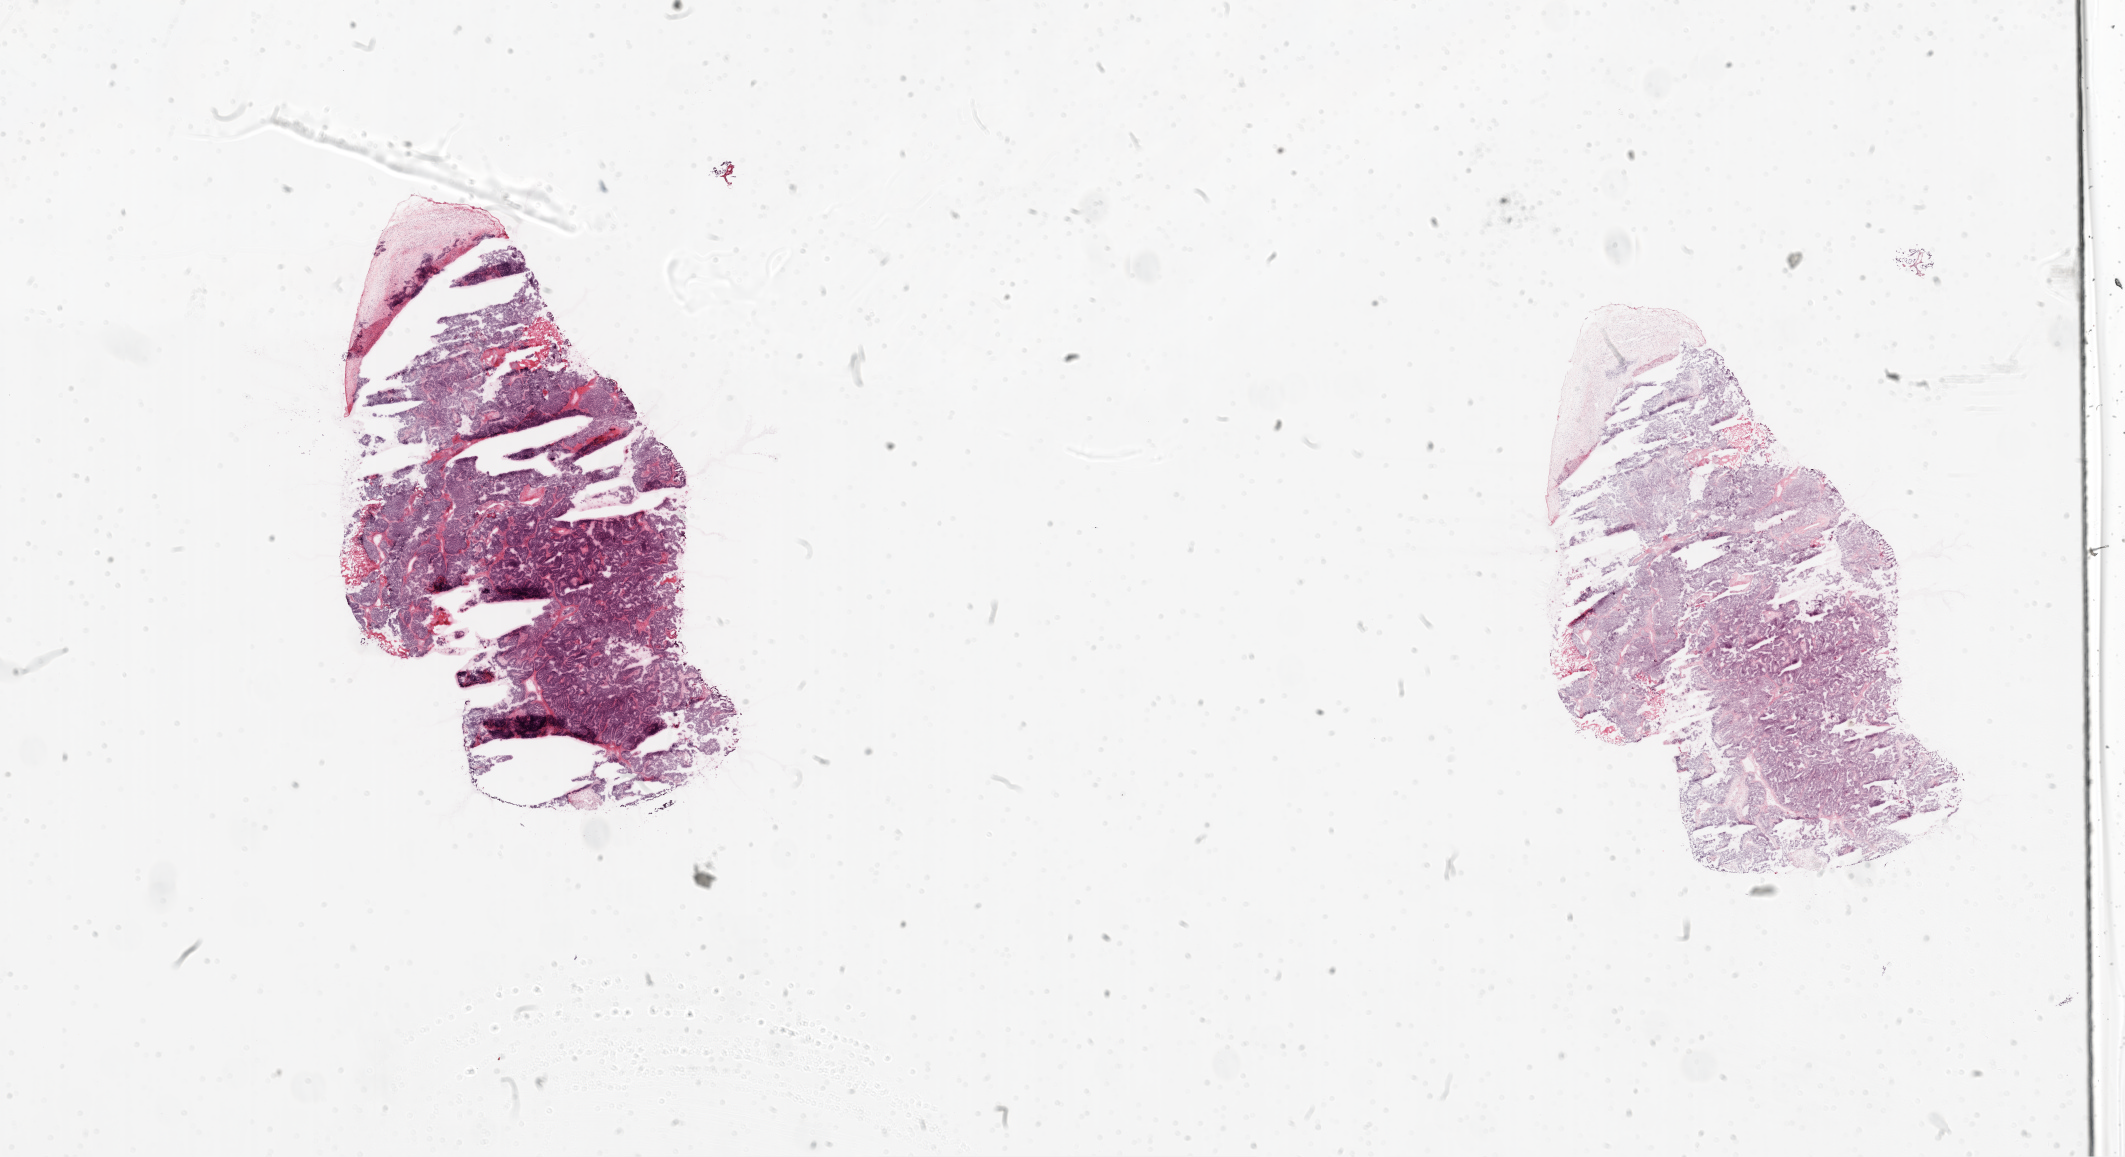
Hematoxylin and eosin (H&E) stained whole-slide image — a low-resolution overview of the entire scanned area, about 34.1 x 18.6 mm, frozen section, primary tumour sample from the ovary. Female, age 64 years at initial diagnosis. Histologic grade: G3 (poorly differentiated). Slide review estimates, as recorded: tumour cells 95%, tumour nuclei 99%, normal cells 0%, stromal cells 5%, necrosis 0%.
* FIGO stage: IIIC
* laterality: left
* pathologic diagnosis: Serous cystadenocarcinoma, NOS